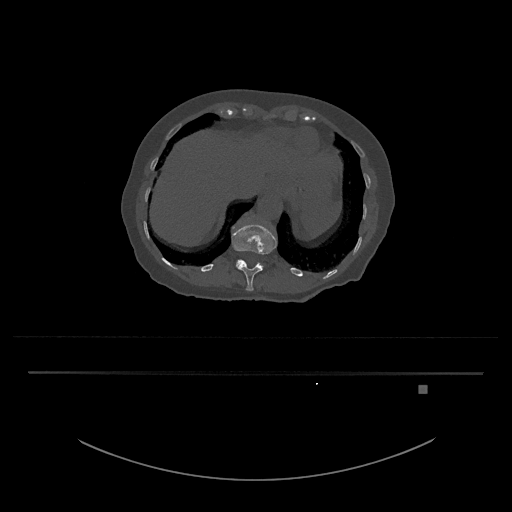
CT including the spine, one axial slice. Slice 599 of 797 in the series (ordered by position). Reconstruction kernel Br40s/3. 120 kVp. Bone window (W 1800 / L 400 HU). 512 × 512 image matrix. Patient: female, 57 years. From the clinical record (not read from this slice): primary cancer: cervical.
Outlined on this slice (semi-automatic segmentation, software-assisted and operator-edited):
- L1 vertebra: box from (x=236, y=260) to (x=264, y=267) px
- T12 vertebra: (x=231, y=223)–(x=277, y=291)